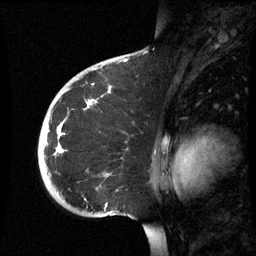
Breast MRI (dynamic contrast-enhanced), one sagittal slice; slice 41 of 60 in the series (ordered by position); dynamic contrast-enhanced series, image 2 of 3 at this slice position (ordered by acquisition); 1.5 T; TE 4.2 ms, TR 8.9 ms; 2.6 mm slice thickness; 256 × 256 image matrix, field of view 220 × 220 mm. Female patient, age 35 years. Case-level facts recorded for this patient, not image findings: setting: breast cancer imaged before/during neoadjuvant chemotherapy; receptor status: HR-positive, HER2-negative.
Structures marked on this image (semi-automatic segmentation, software-assisted and operator-edited):
- analysis volume of interest (the breast-tissue region the enhancement analysis was run in; not a lesion): bounding box [x1, y1, x2, y2] px = [38, 74, 152, 219]
- tumour enhancement mask (voxels above the 70 % enhancement threshold inside the analysis volume of interest): [55, 100, 92, 155]